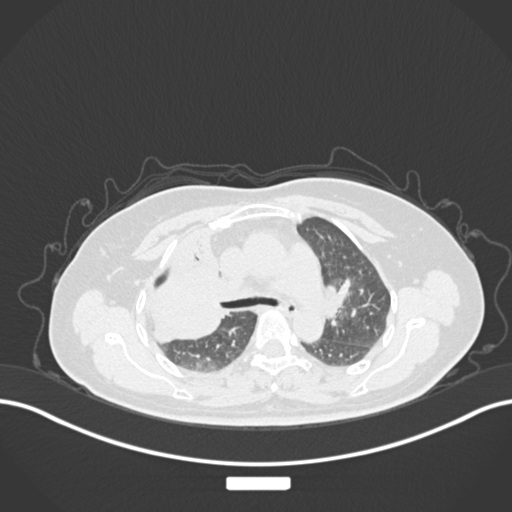
Chest CT, one axial slice. Position 102 of 177 along the scan axis. Reconstruction kernel B30f. Lung window (W 1500 / L -600 HU). 1 mm slice thickness. 512 × 512 image matrix, field of view 400 × 400 mm. Patient: female, 60 years. From the clinical record (not read from this slice): clinical TNM (as recorded): T3 N1 M1.
Outlined on this slice (bounding box drawn by a radiologist):
- lung tumour (recorded histology: adenocarcinoma): bounding box (x1, y1, x2, y2) in pixels: (145, 250, 234, 351)